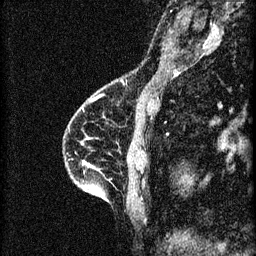
Breast MRI (dynamic contrast-enhanced), one sagittal slice; slice 21 of 60 in the series (ordered by position); 3 images stored at this slice position (order not interpretable as contrast timing); 1.5 T; TE 4.2 ms, TR 8.2 ms; 2 mm slice thickness; 256 × 256 image matrix, field of view 180 × 180 mm. Patient: female, 46 years.
Annotated regions visible in this slice (semi-automatic segmentation, software-assisted and operator-edited):
- analysis volume of interest (the breast-tissue region the enhancement analysis was run in; not a lesion): bounding box [x1, y1, x2, y2] px = [64, 114, 148, 209]
- tumour enhancement mask (voxels above the 70 % enhancement threshold inside the analysis volume of interest): [84, 162, 86, 187]